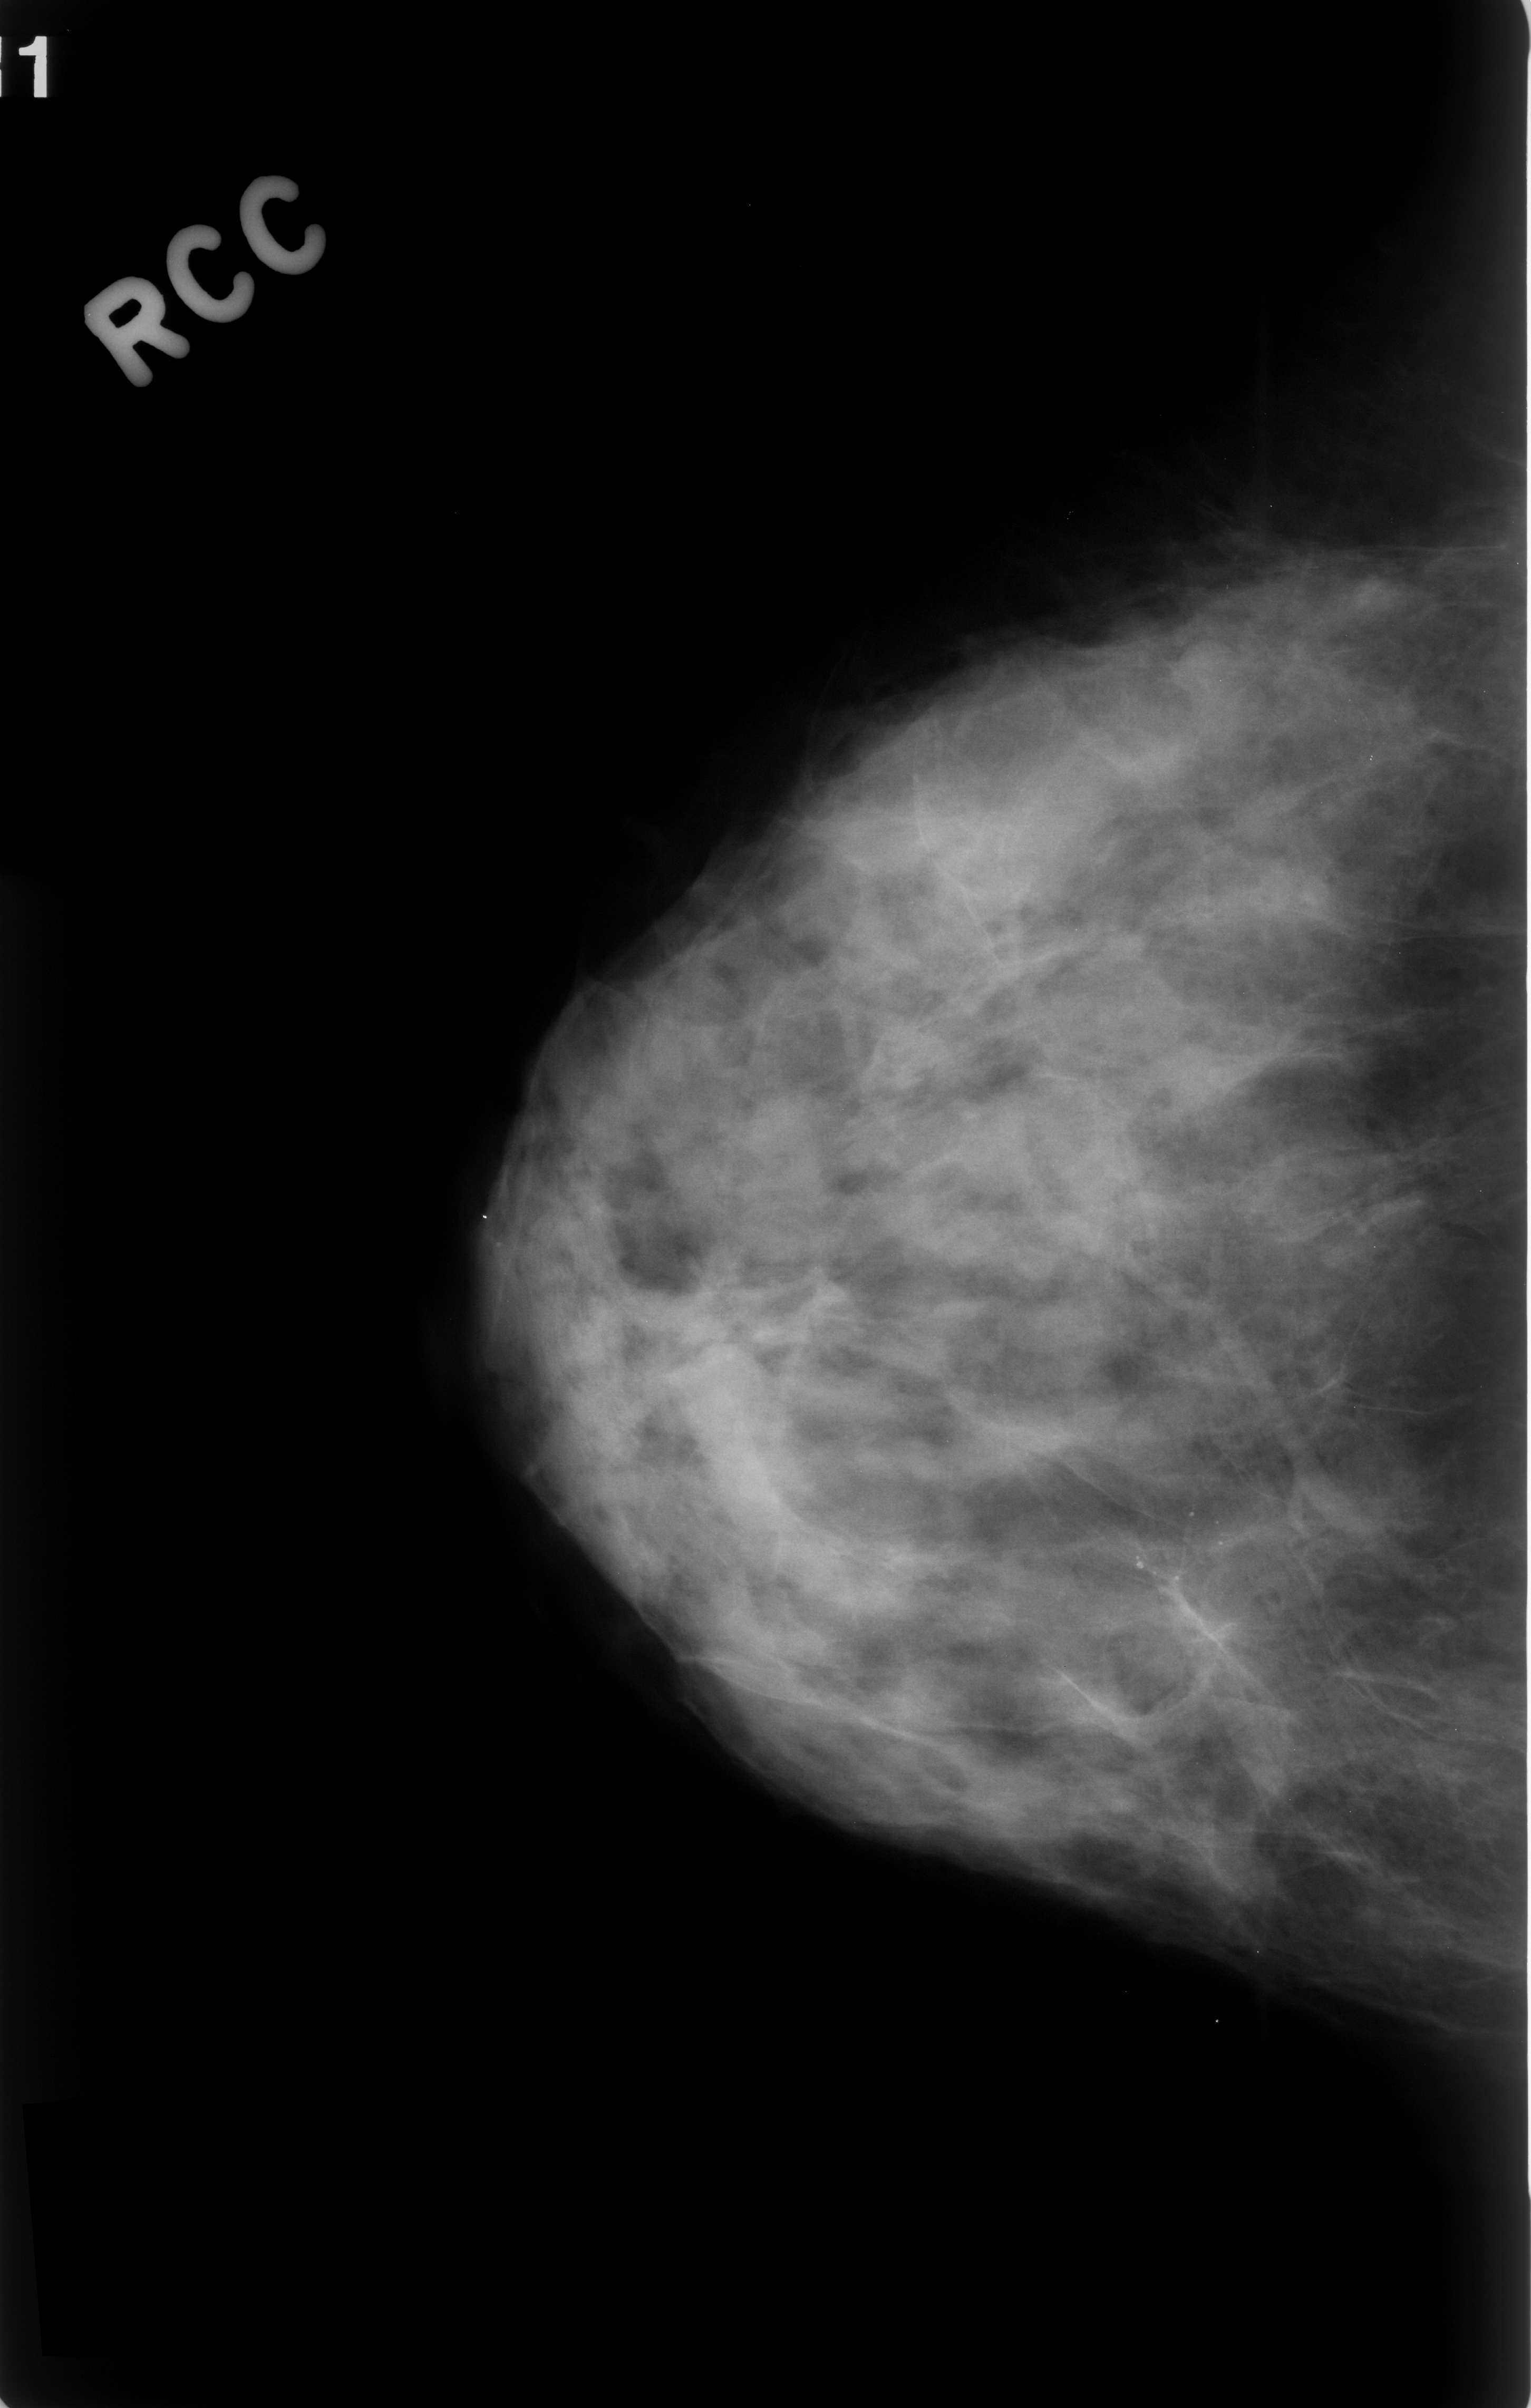
Digitized screen-film mammogram; right breast; craniocaudal (CC) view; BI-RADS breast density category 3 (scale 1–4).
Calcifications, morphology round and regular, distribution clustered; BI-RADS assessment category 4; pathology (as recorded): benign.